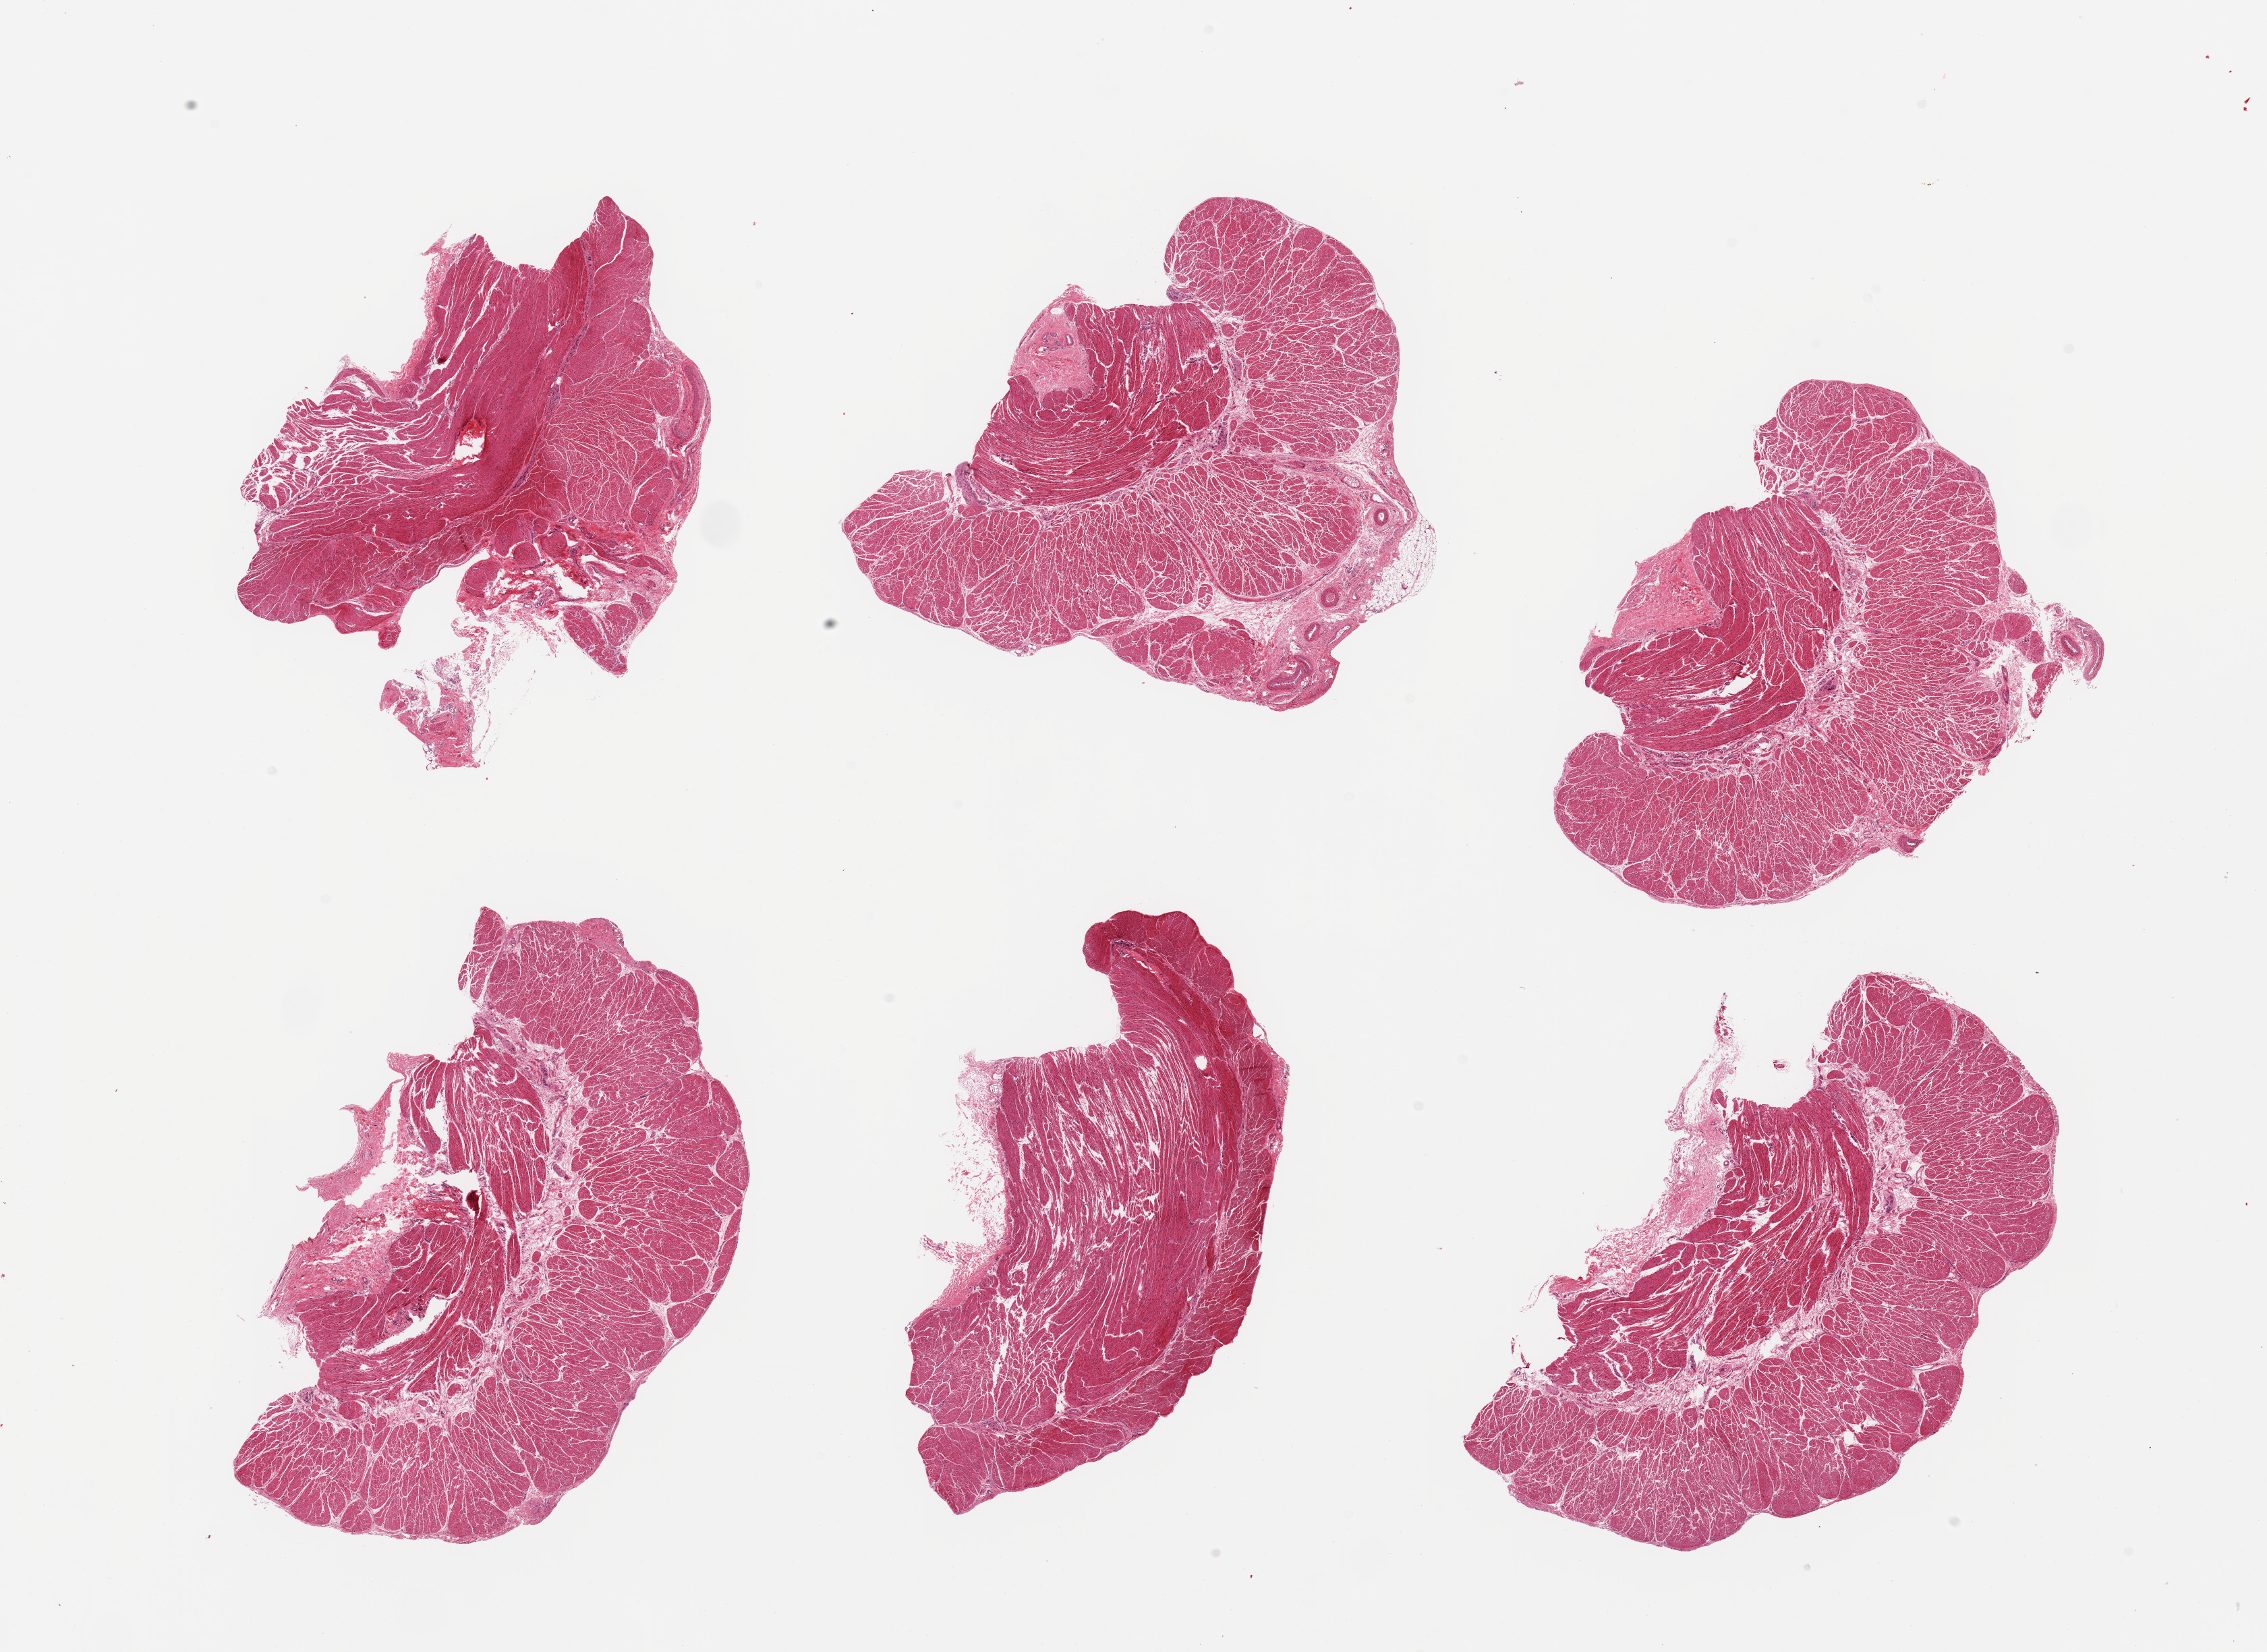
Digitized hematoxylin and eosin (H&E)-stained section, whole scanned area (about 26.6 x 19.4 mm, acquisition: 20x scan) shown as a low-resolution overview; PAXgene-fixed paraffin-embedded (PFPE) section; sampled site (target tissue): esophageal muscle; tissue donor sample. Donor: female.
Reviewer comment on this tissue sample: 6 pieces, all muscularis, good specimens.